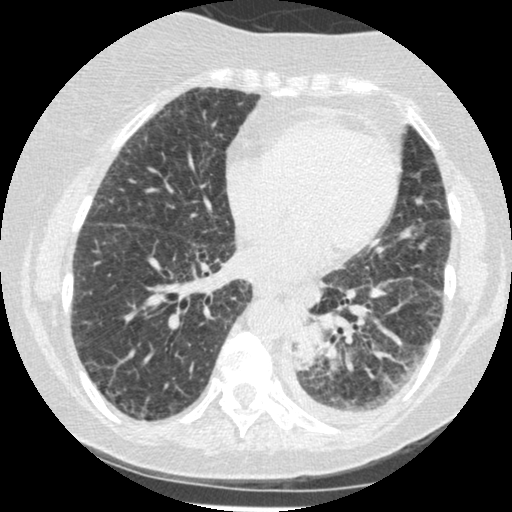
Low-dose screening chest CT, one axial slice; position 82 of 341 along the scan axis; 120 kVp; lung window (W 1500 / L -600 HU); 1.25 mm slice thickness; 512 × 512 image matrix.
Annotated regions visible in this slice (manually delineated by an expert):
- lesion 1 (tumor, lower lobe of left lung): bounding box [x1, y1, x2, y2] px = [292, 322, 322, 370]